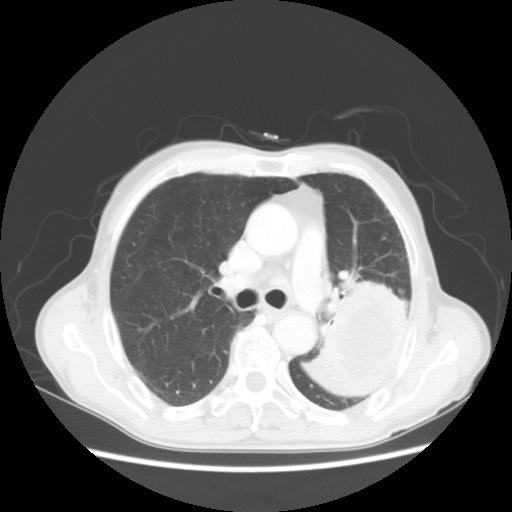
Chest CT, one axial slice. Position 32 of 51 along the scan axis. Reconstruction kernel STANDARD. Lung window (W 1500 / L -600 HU). 5 mm slice thickness. 512 × 512 image matrix, field of view 360 × 360 mm. Patient: male, 64 years. From the clinical record (not read from this slice): clinical TNM (as recorded): T4 N0 M0.
Outlined on this slice (rectangle marked by the reading radiologist):
- lung tumour (recorded histology: squamous cell carcinoma): bounding box [x1, y1, x2, y2] px = [302, 263, 416, 411]